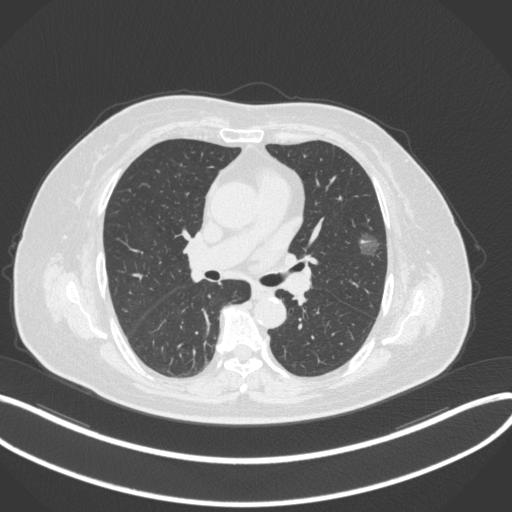
Chest CT, one axial slice. Position 177 of 286 along the scan axis. 120 kVp. Lung window (W 1500 / L -600 HU). 1 mm slice thickness. 512 × 512 image matrix, field of view 400 × 400 mm. Patient: female, 76 years. Case-level facts recorded for this patient, not image findings: clinical TNM (as recorded): T1b N0 M0; histopathological grade: G1-2.
Annotated regions visible in this slice (rectangle marked by the reading radiologist):
- lung tumour (recorded histology: adenocarcinoma): bounding box [x1, y1, x2, y2] px = [351, 229, 381, 262]